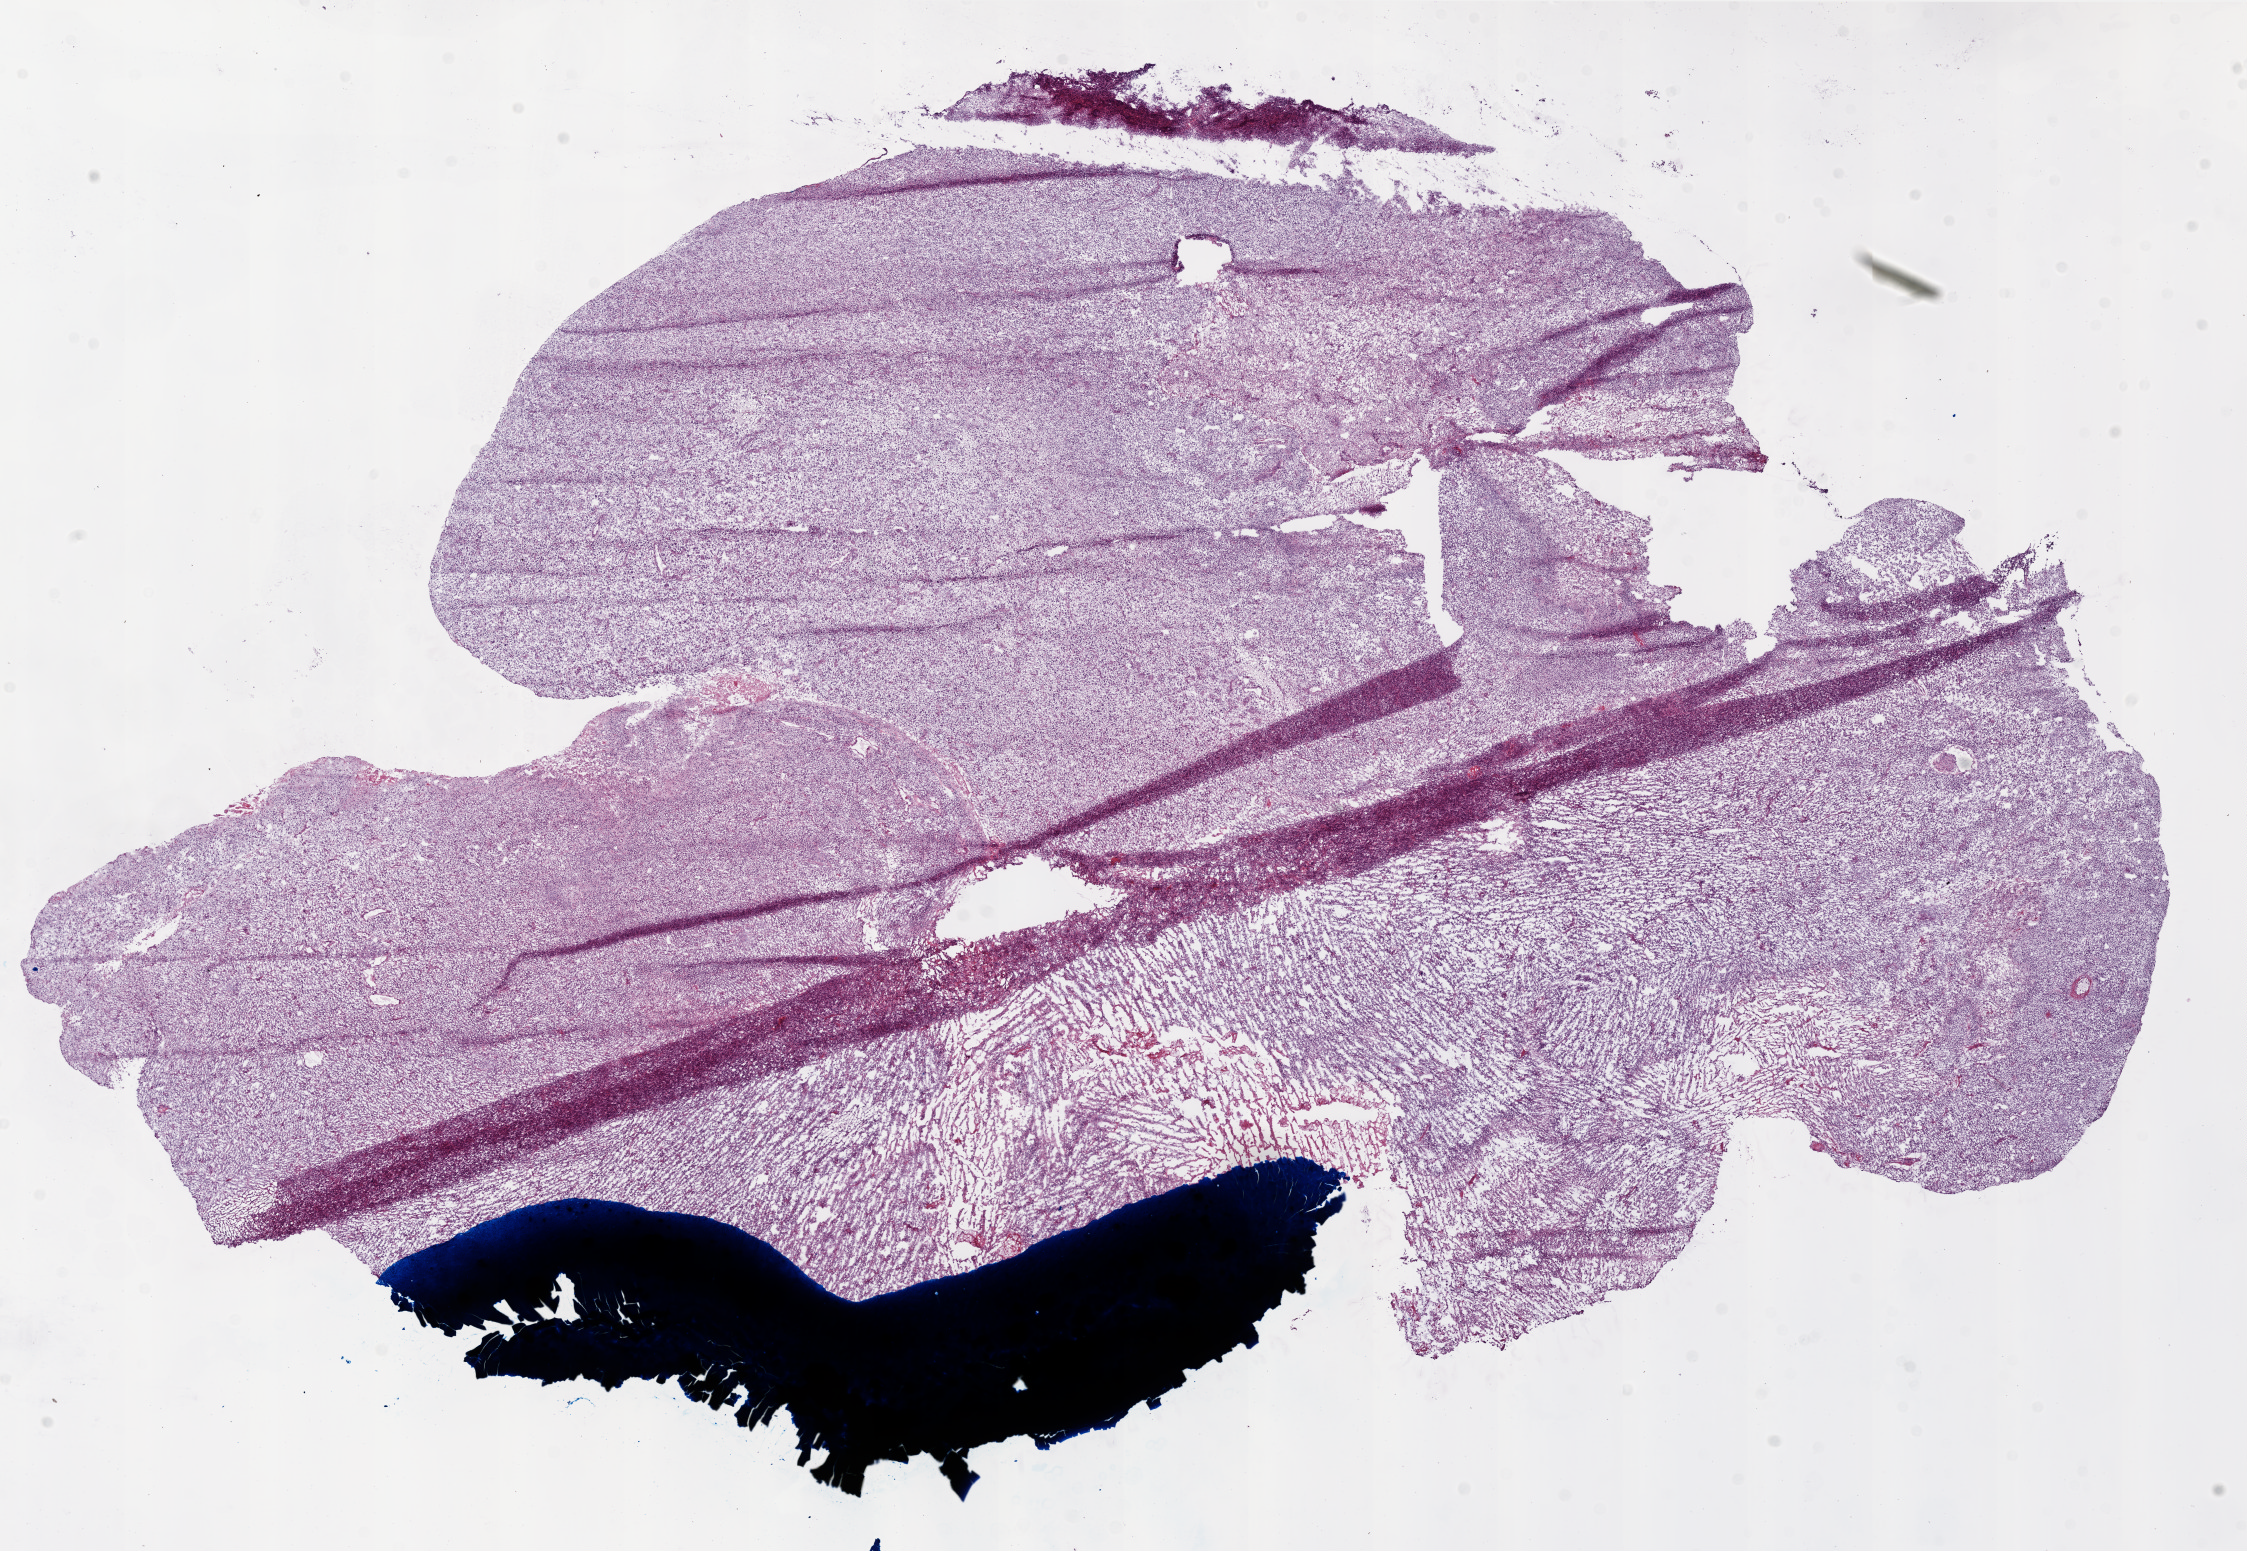
Whole-slide histology image, H&E, a low-resolution overview of the entire scanned area, about 18.0 x 12.4 mm; frozen section; sample: primary tumour, brain. Female, age 67 years at initial diagnosis. Slide review estimates, as recorded: tumour cells 90%, tumour nuclei 100%, normal cells 0%, stromal cells 0%, necrosis 10%.
* diagnosis: Glioblastoma